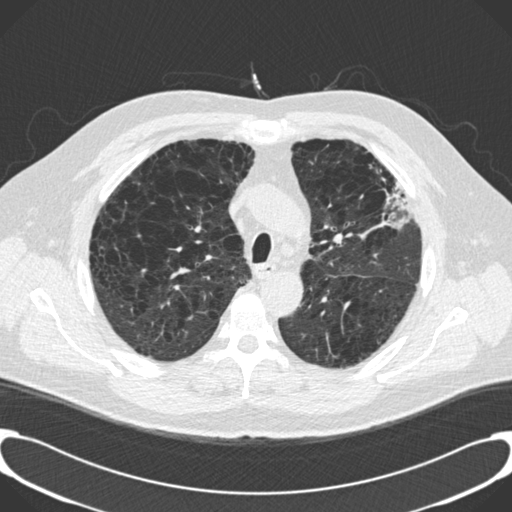
Low-dose screening chest CT, one axial slice; slice 144 of 189 in the series (ordered by position); reconstruction kernel B30f; 120 kVp; lung window (W 1500 / L -600 HU); 2 mm slice thickness; 512 × 512 image matrix, field of view 380 × 380 mm.
Annotated regions visible in this slice (outlined manually by an expert reader):
- lesion 1 (tumor, upper lobe of left lung): bounding box <384,184,411,229> (left, top, right, bottom; pixels)